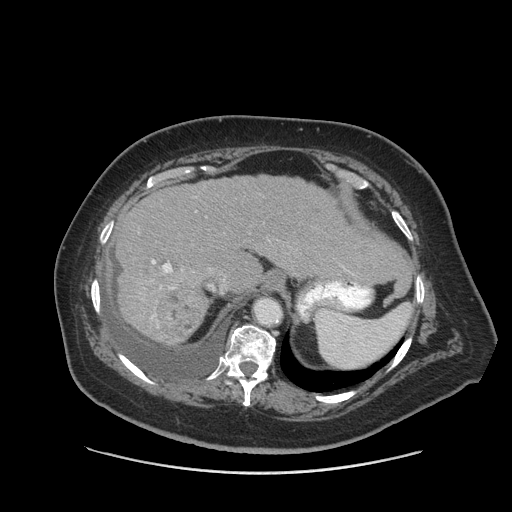
Contrast-enhanced abdominal CT (liver protocol), one axial slice. Slice 64 of 91 in the series (ordered by position). Reconstruction kernel STANDARD. 140 kVp. Soft-tissue window (W 400 / L 40 HU). 512 × 512 image matrix, field of view 420 × 420 mm. From the clinical record (not read from this slice): diagnosis: hepatocellular carcinoma (patient treated with transarterial chemoembolisation; whether this scan precedes or follows treatment is not stated here); TNM stage (as recorded): Stage-I; Child-Pugh class: A; tumour differentiation: well differentiated; tumour nodularity: uninodular.
Outlined on this slice (semi-automatically segmented with operator editing):
- liver parenchyma outside the tumour (the mass and vessels are separate outlines, so this box may not span the whole liver): box from (x=116, y=174) to (x=404, y=342) px
- mass: (x=156, y=287)–(x=209, y=346)
- liver vessels: (x=152, y=260)–(x=173, y=318)